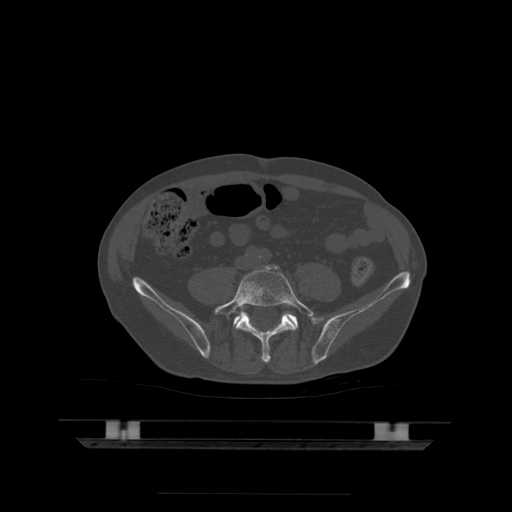
CT including the spine, one axial slice. Position 72 of 522 along the scan axis. Bone window (W 1800 / L 400 HU). 512 × 512 image matrix, field of view 436 × 436 mm. Patient age 68 years. Case-level facts recorded for this patient, not image findings: primary cancer: urothelial.
Structures marked on this image (semi-automatic segmentation, software-assisted and operator-edited):
- L5 vertebra: box from (x=214, y=265) to (x=314, y=363) px